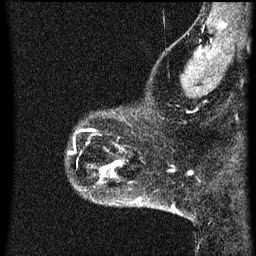
Breast MRI (dynamic contrast-enhanced), one sagittal slice; dynamic contrast-enhanced series, image 2 of 3 at this slice position (ordered by acquisition); 1.5 T; TE 4.2 ms, TR 8 ms; 2 mm slice thickness; 256 × 256 image matrix, field of view 180 × 180 mm. Patient: female, 43 years.
Outlined on this slice (semi-automatic segmentation, software-assisted and operator-edited):
- analysis volume of interest (the breast-tissue region the enhancement analysis was run in; not a lesion): box from (x=68, y=110) to (x=104, y=153) px
- tumour enhancement mask (voxels above the 70 % enhancement threshold inside the analysis volume of interest): (x=68, y=128)–(x=94, y=153)